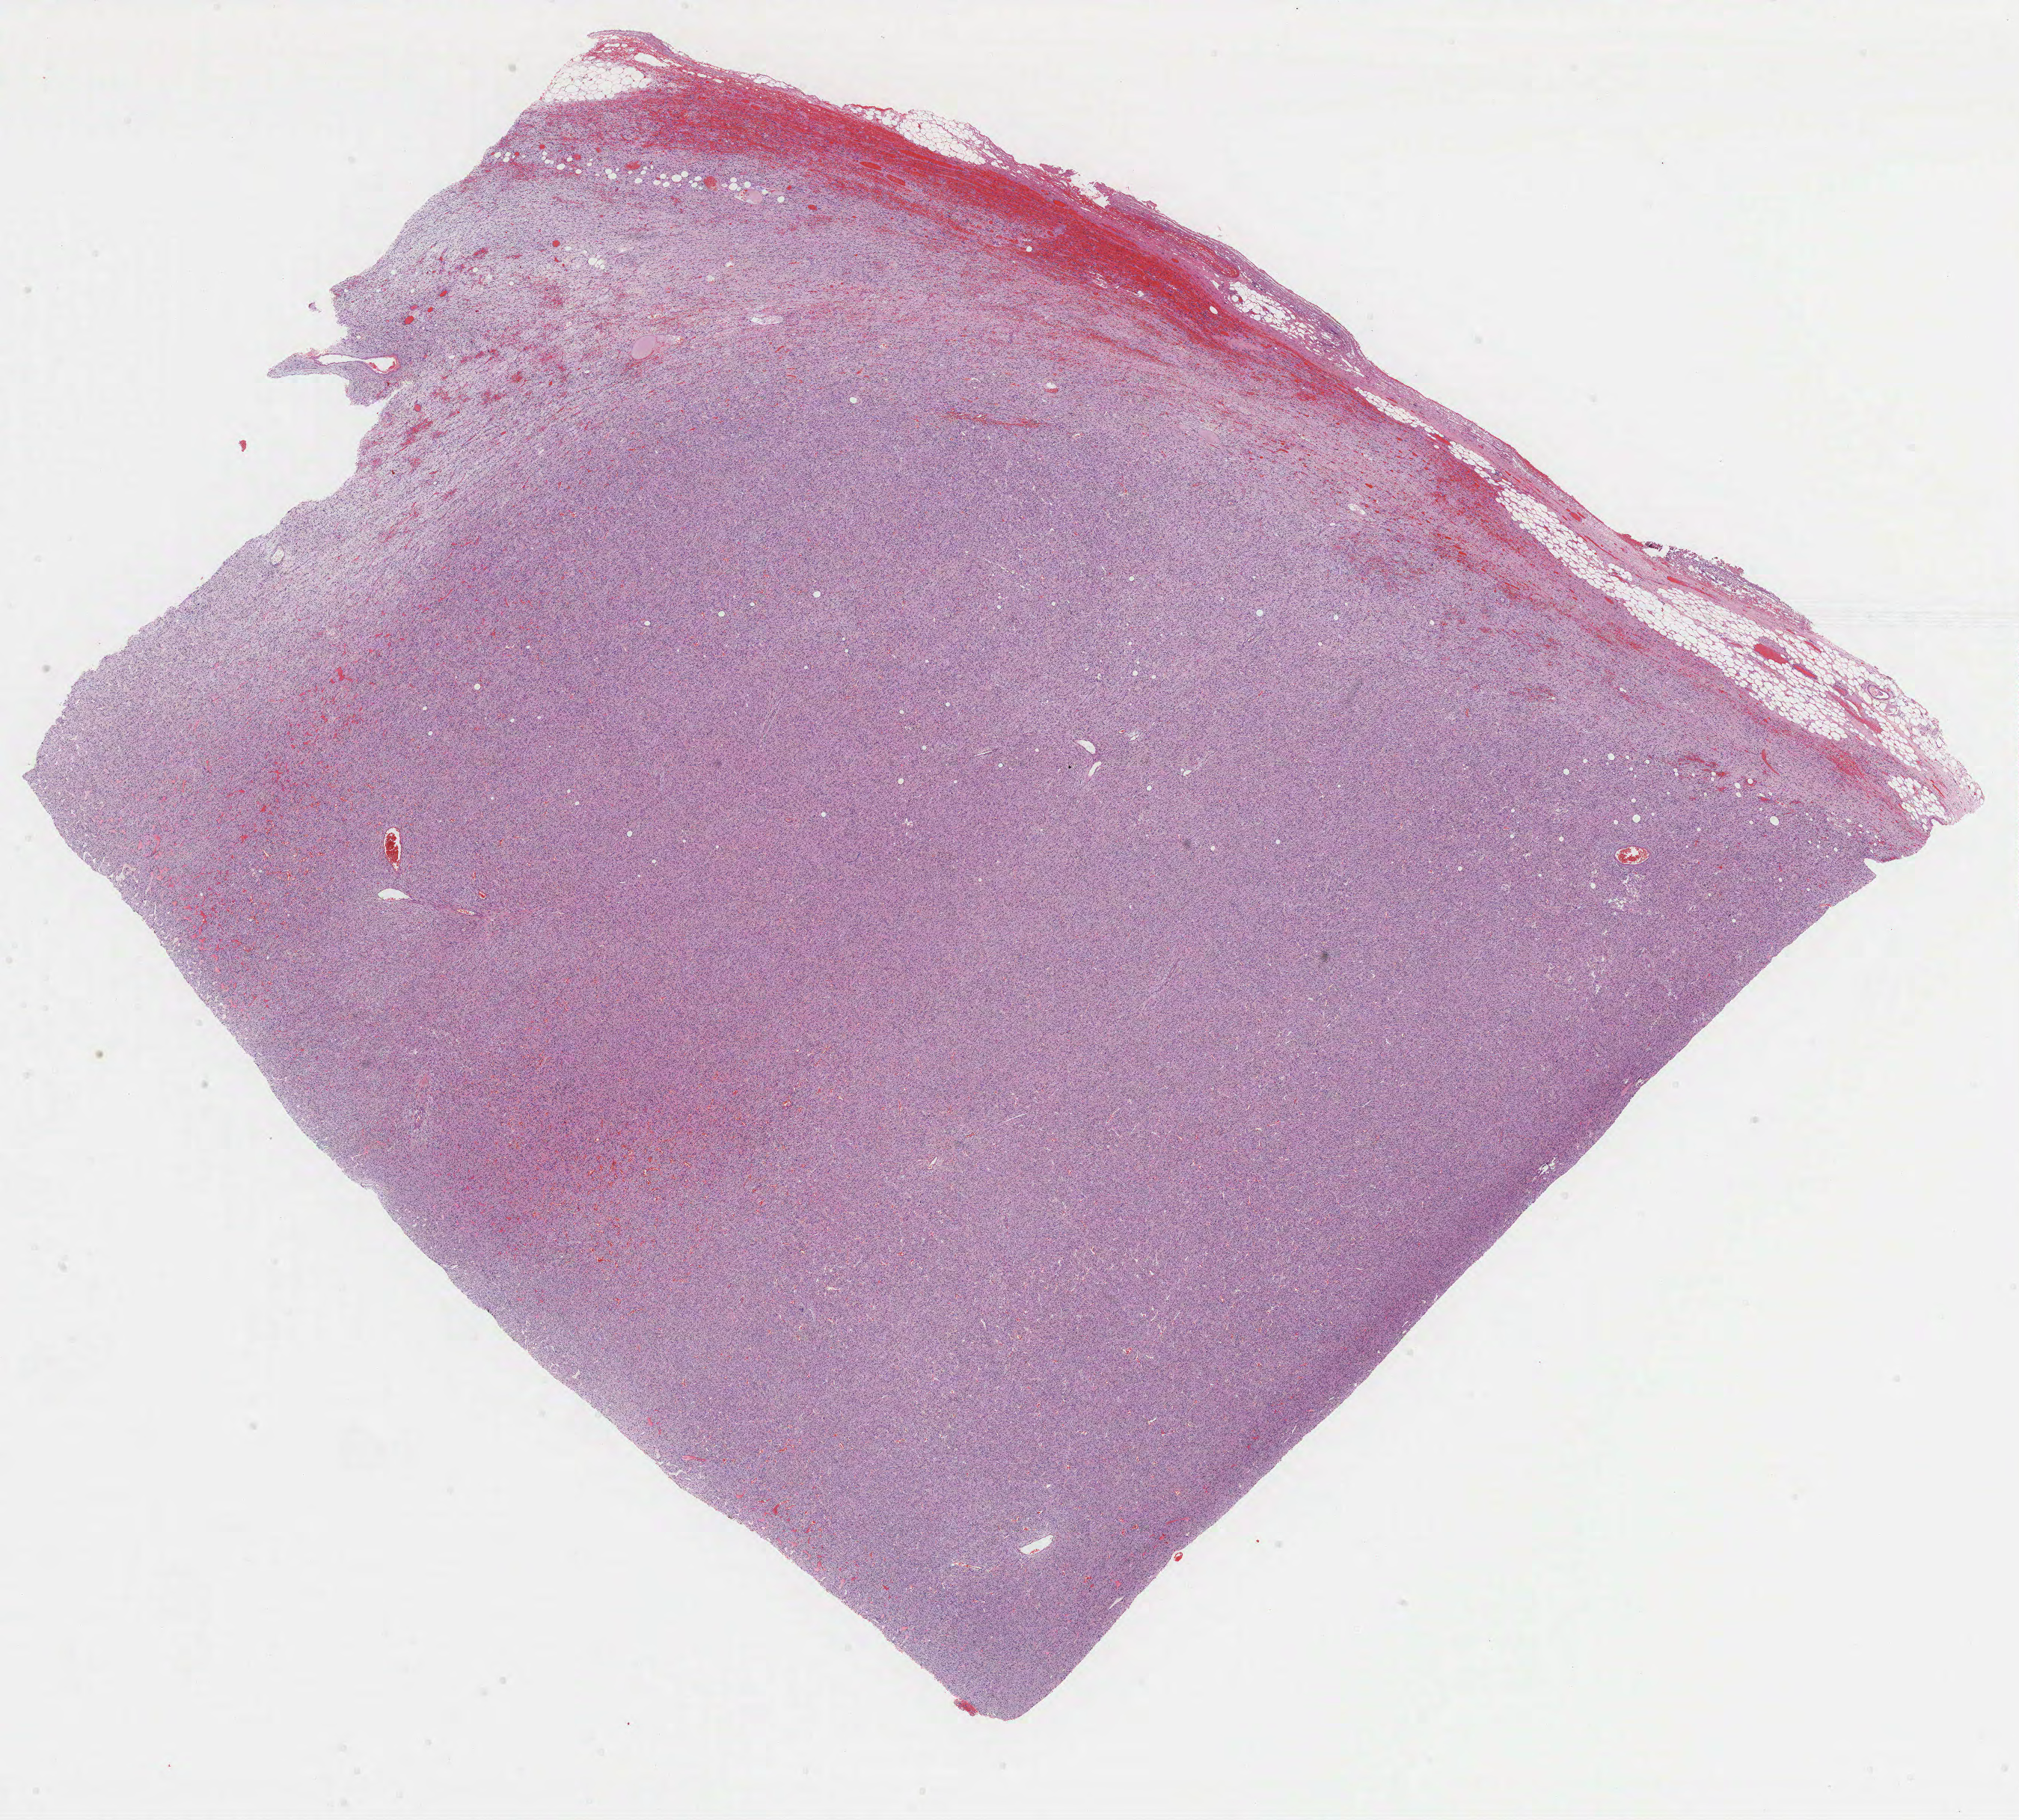
H&E whole-slide image — whole scanned area (about 21.8 x 19.7 mm) shown as a low-resolution overview, formalin-fixed paraffin-embedded (FFPE) diagnostic section, primary tumour sample from the retroperitoneum and peritoneum. Male patient; age at initial diagnosis 67 years.
* histologic diagnosis: Dedifferentiated liposarcoma (specified parts of peritoneum)